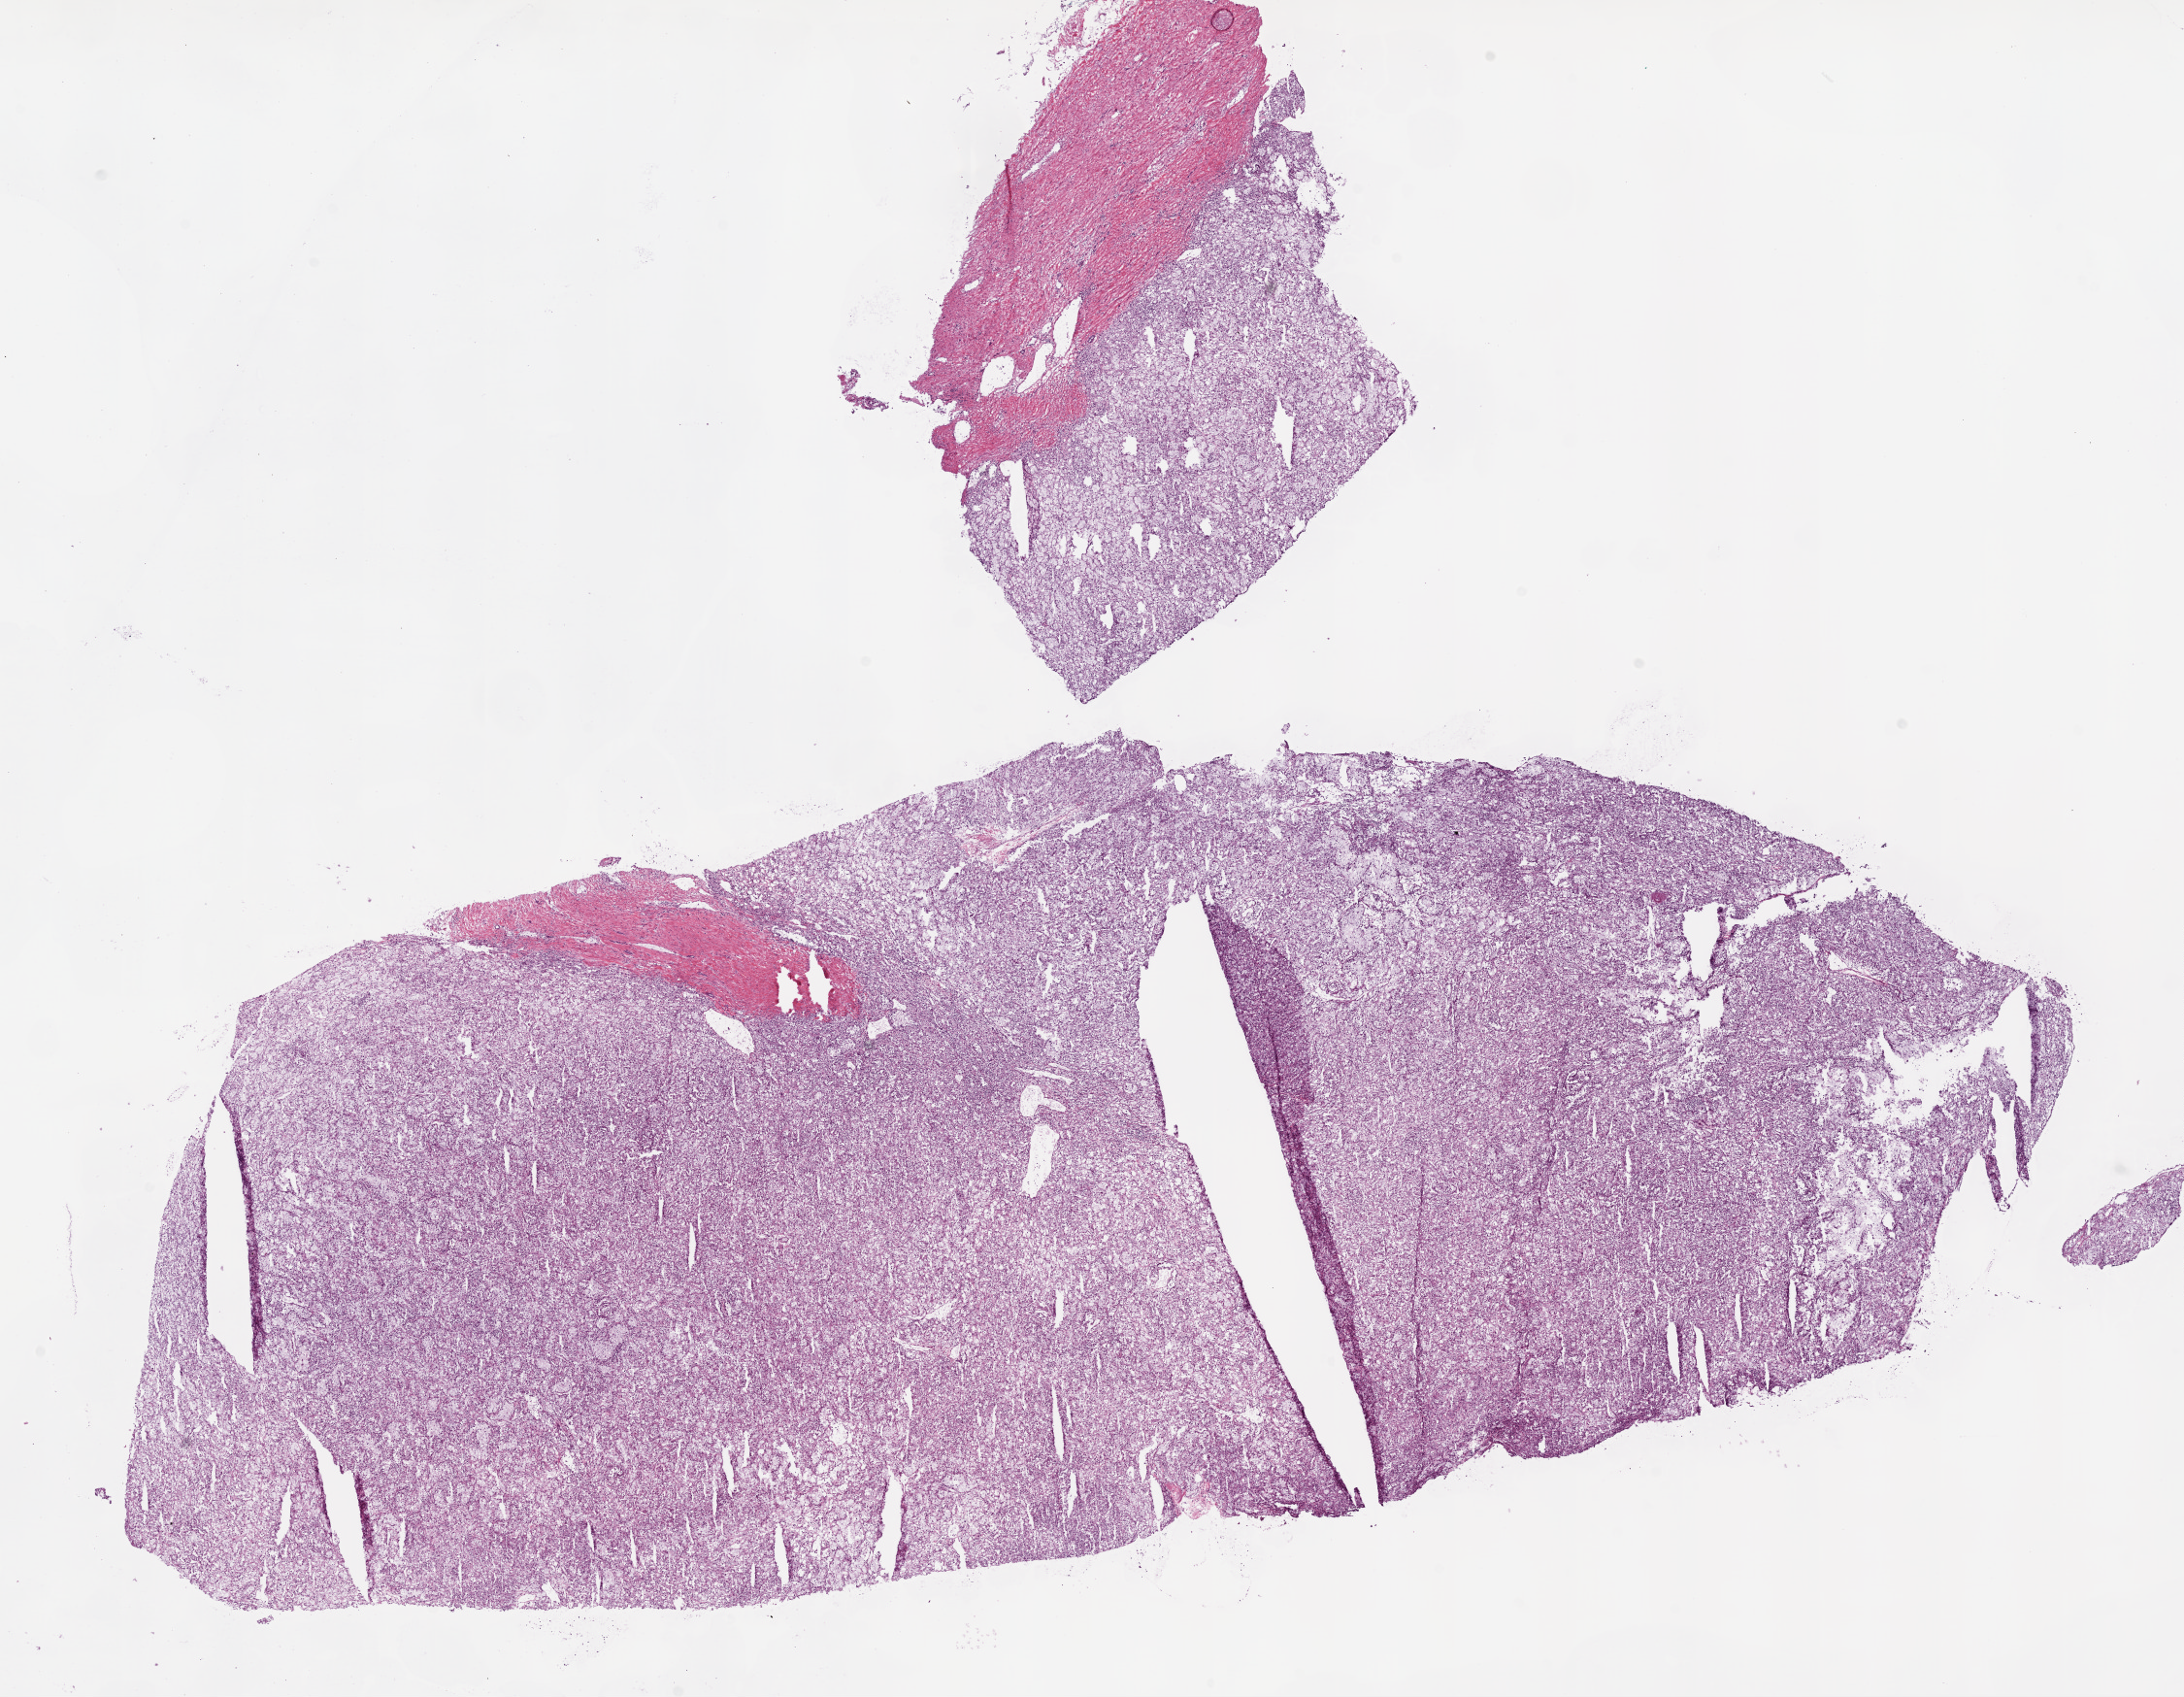
Digitized Hematoxylin and eosin (H&E) stained tissue section (whole slide), a low-resolution overview of the entire scanned area, about 18.1 x 14.0 mm (acquisition: 20x scan), frozen section from the bottom of the tissue portion, primary tumour sample from the kidney. Male, age 50 years at initial diagnosis. Histologic grade: G2 (moderately differentiated). Slide review estimates, as recorded: tumour cells 85%, tumour nuclei 85%, normal cells 0%, stromal cells 15%, necrosis 0%.
• laterality: right
• diagnosis: Clear cell adenocarcinoma, NOS
• AJCC pathologic stage: I